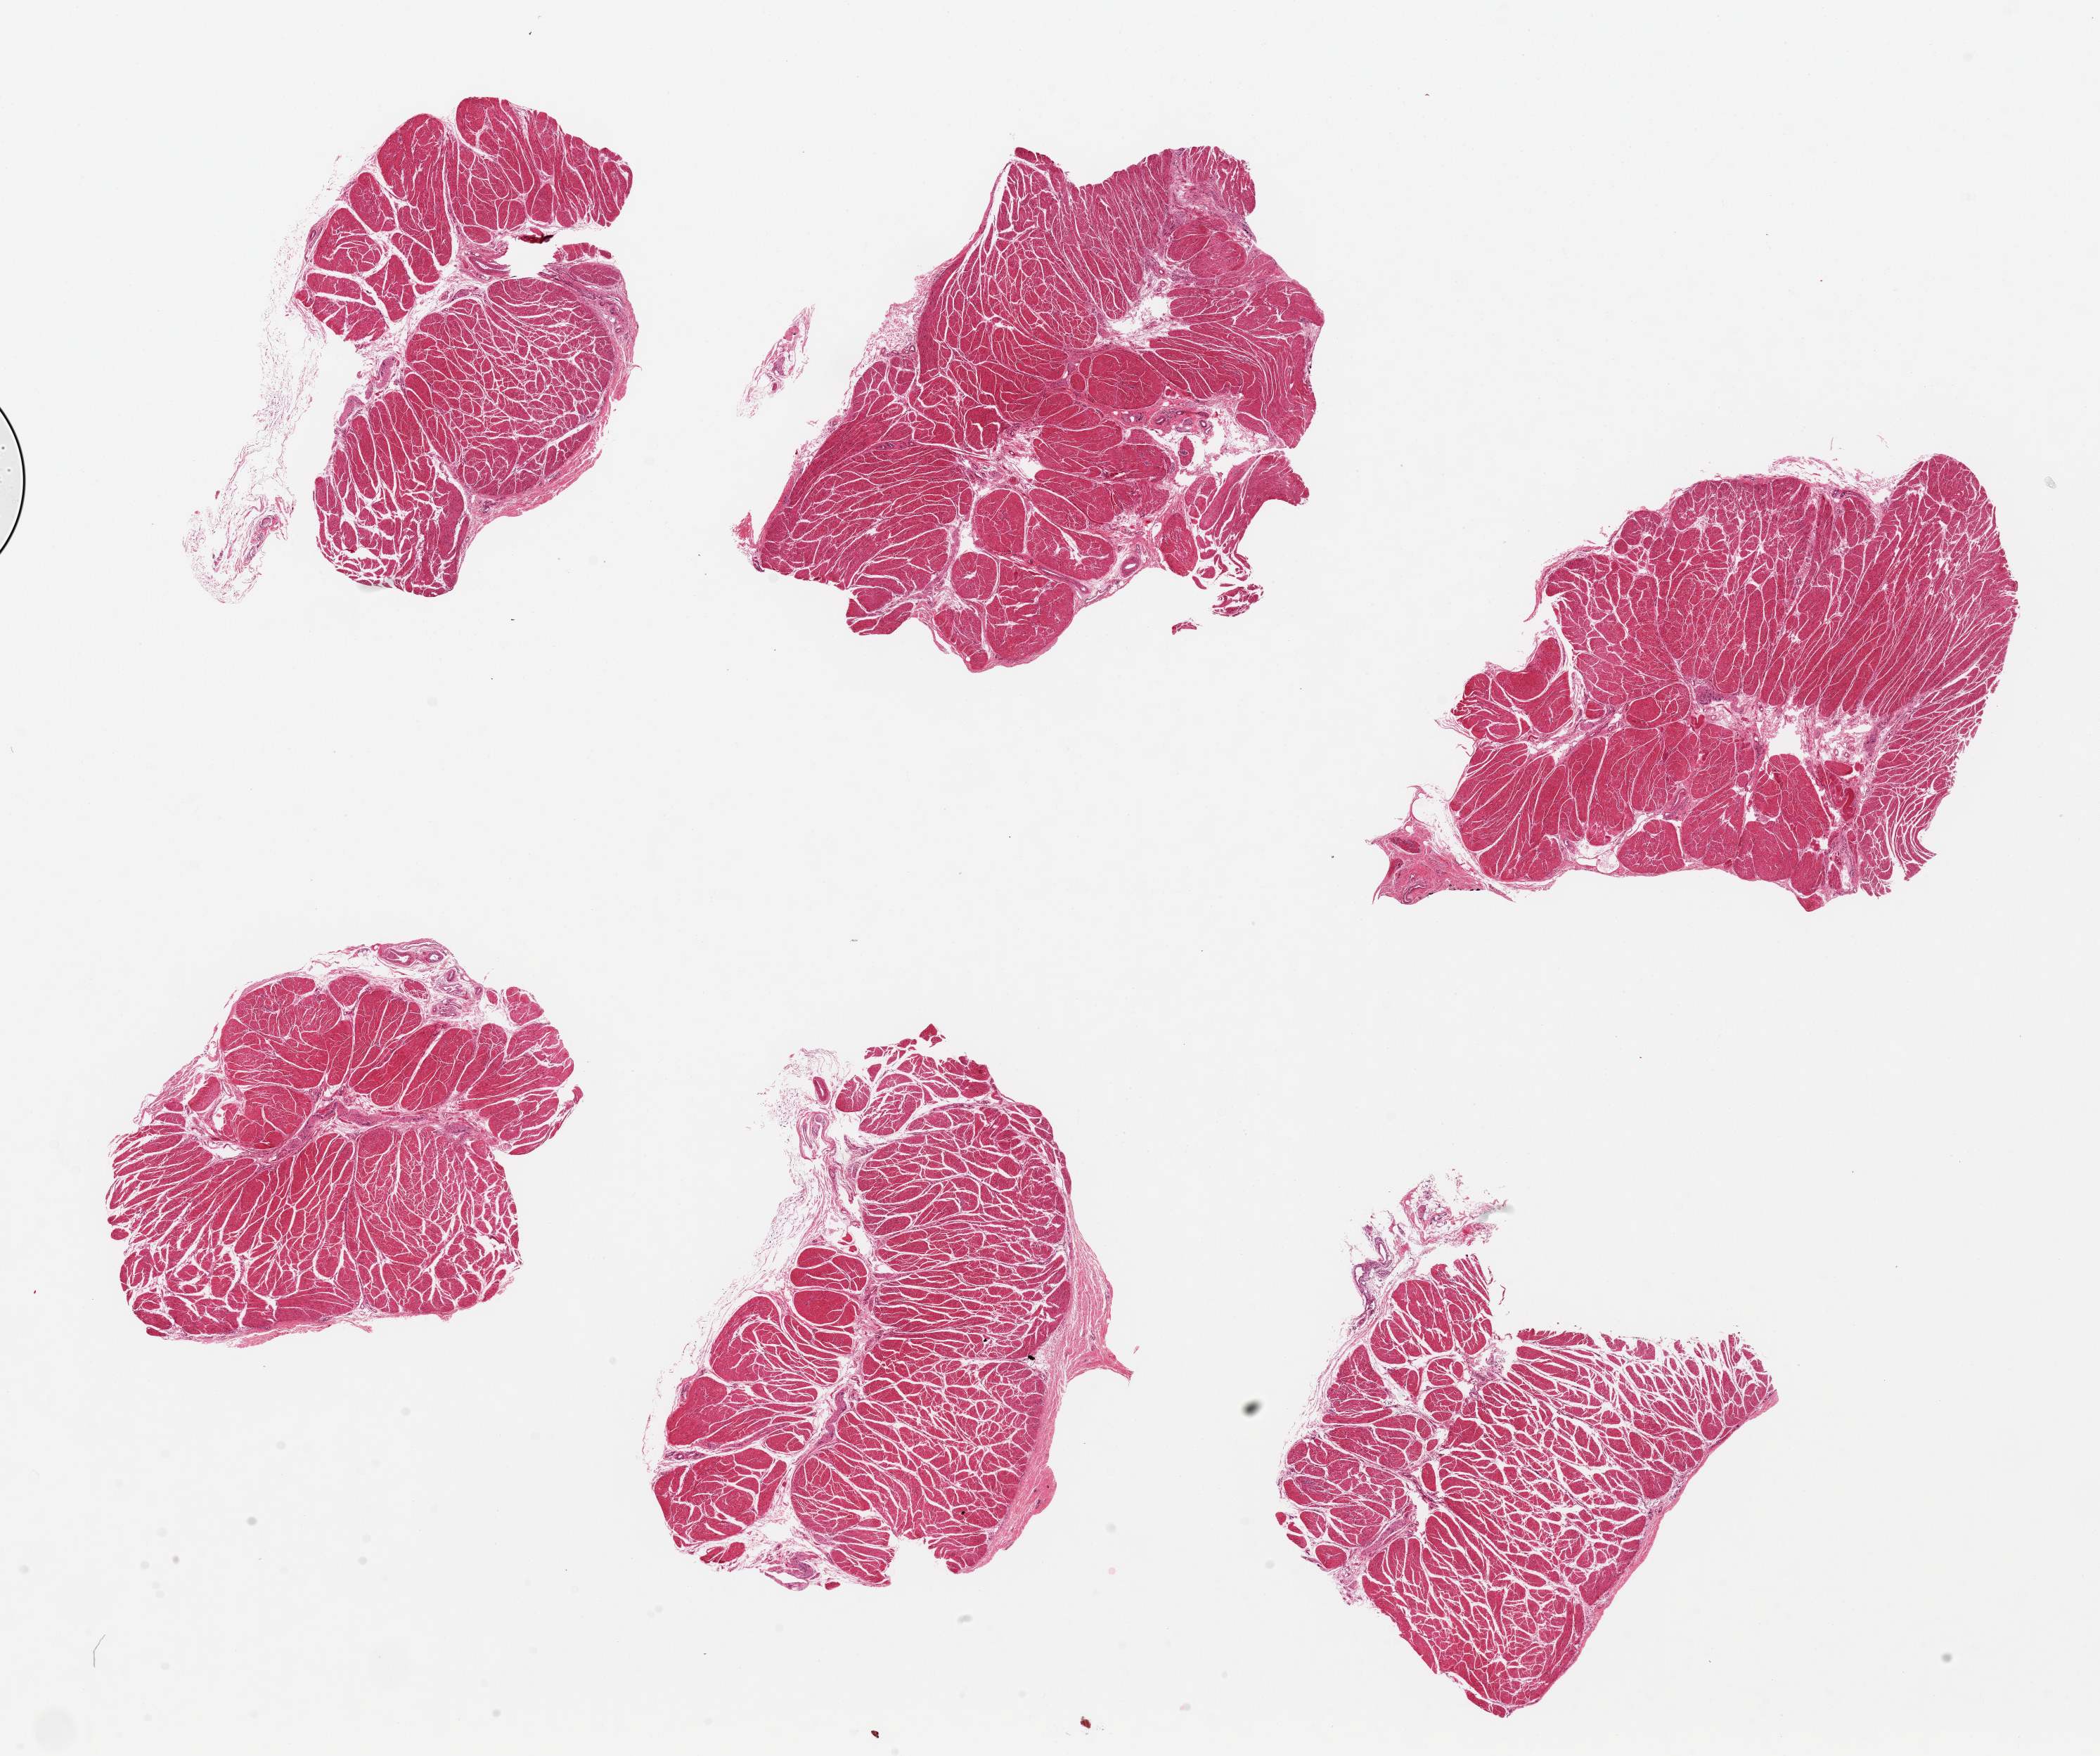
Digitized H&E-stained section, low-resolution overview of the scanned area, about 23.6 x 19.8 mm. PAXgene-fixed, paraffin-embedded tissue. Target tissue: esophageal muscle. Tissue donor sample. Donor sex: male.
Review note (as recorded): 6 pieces, up to 7x6mm; well sampled muscularis.